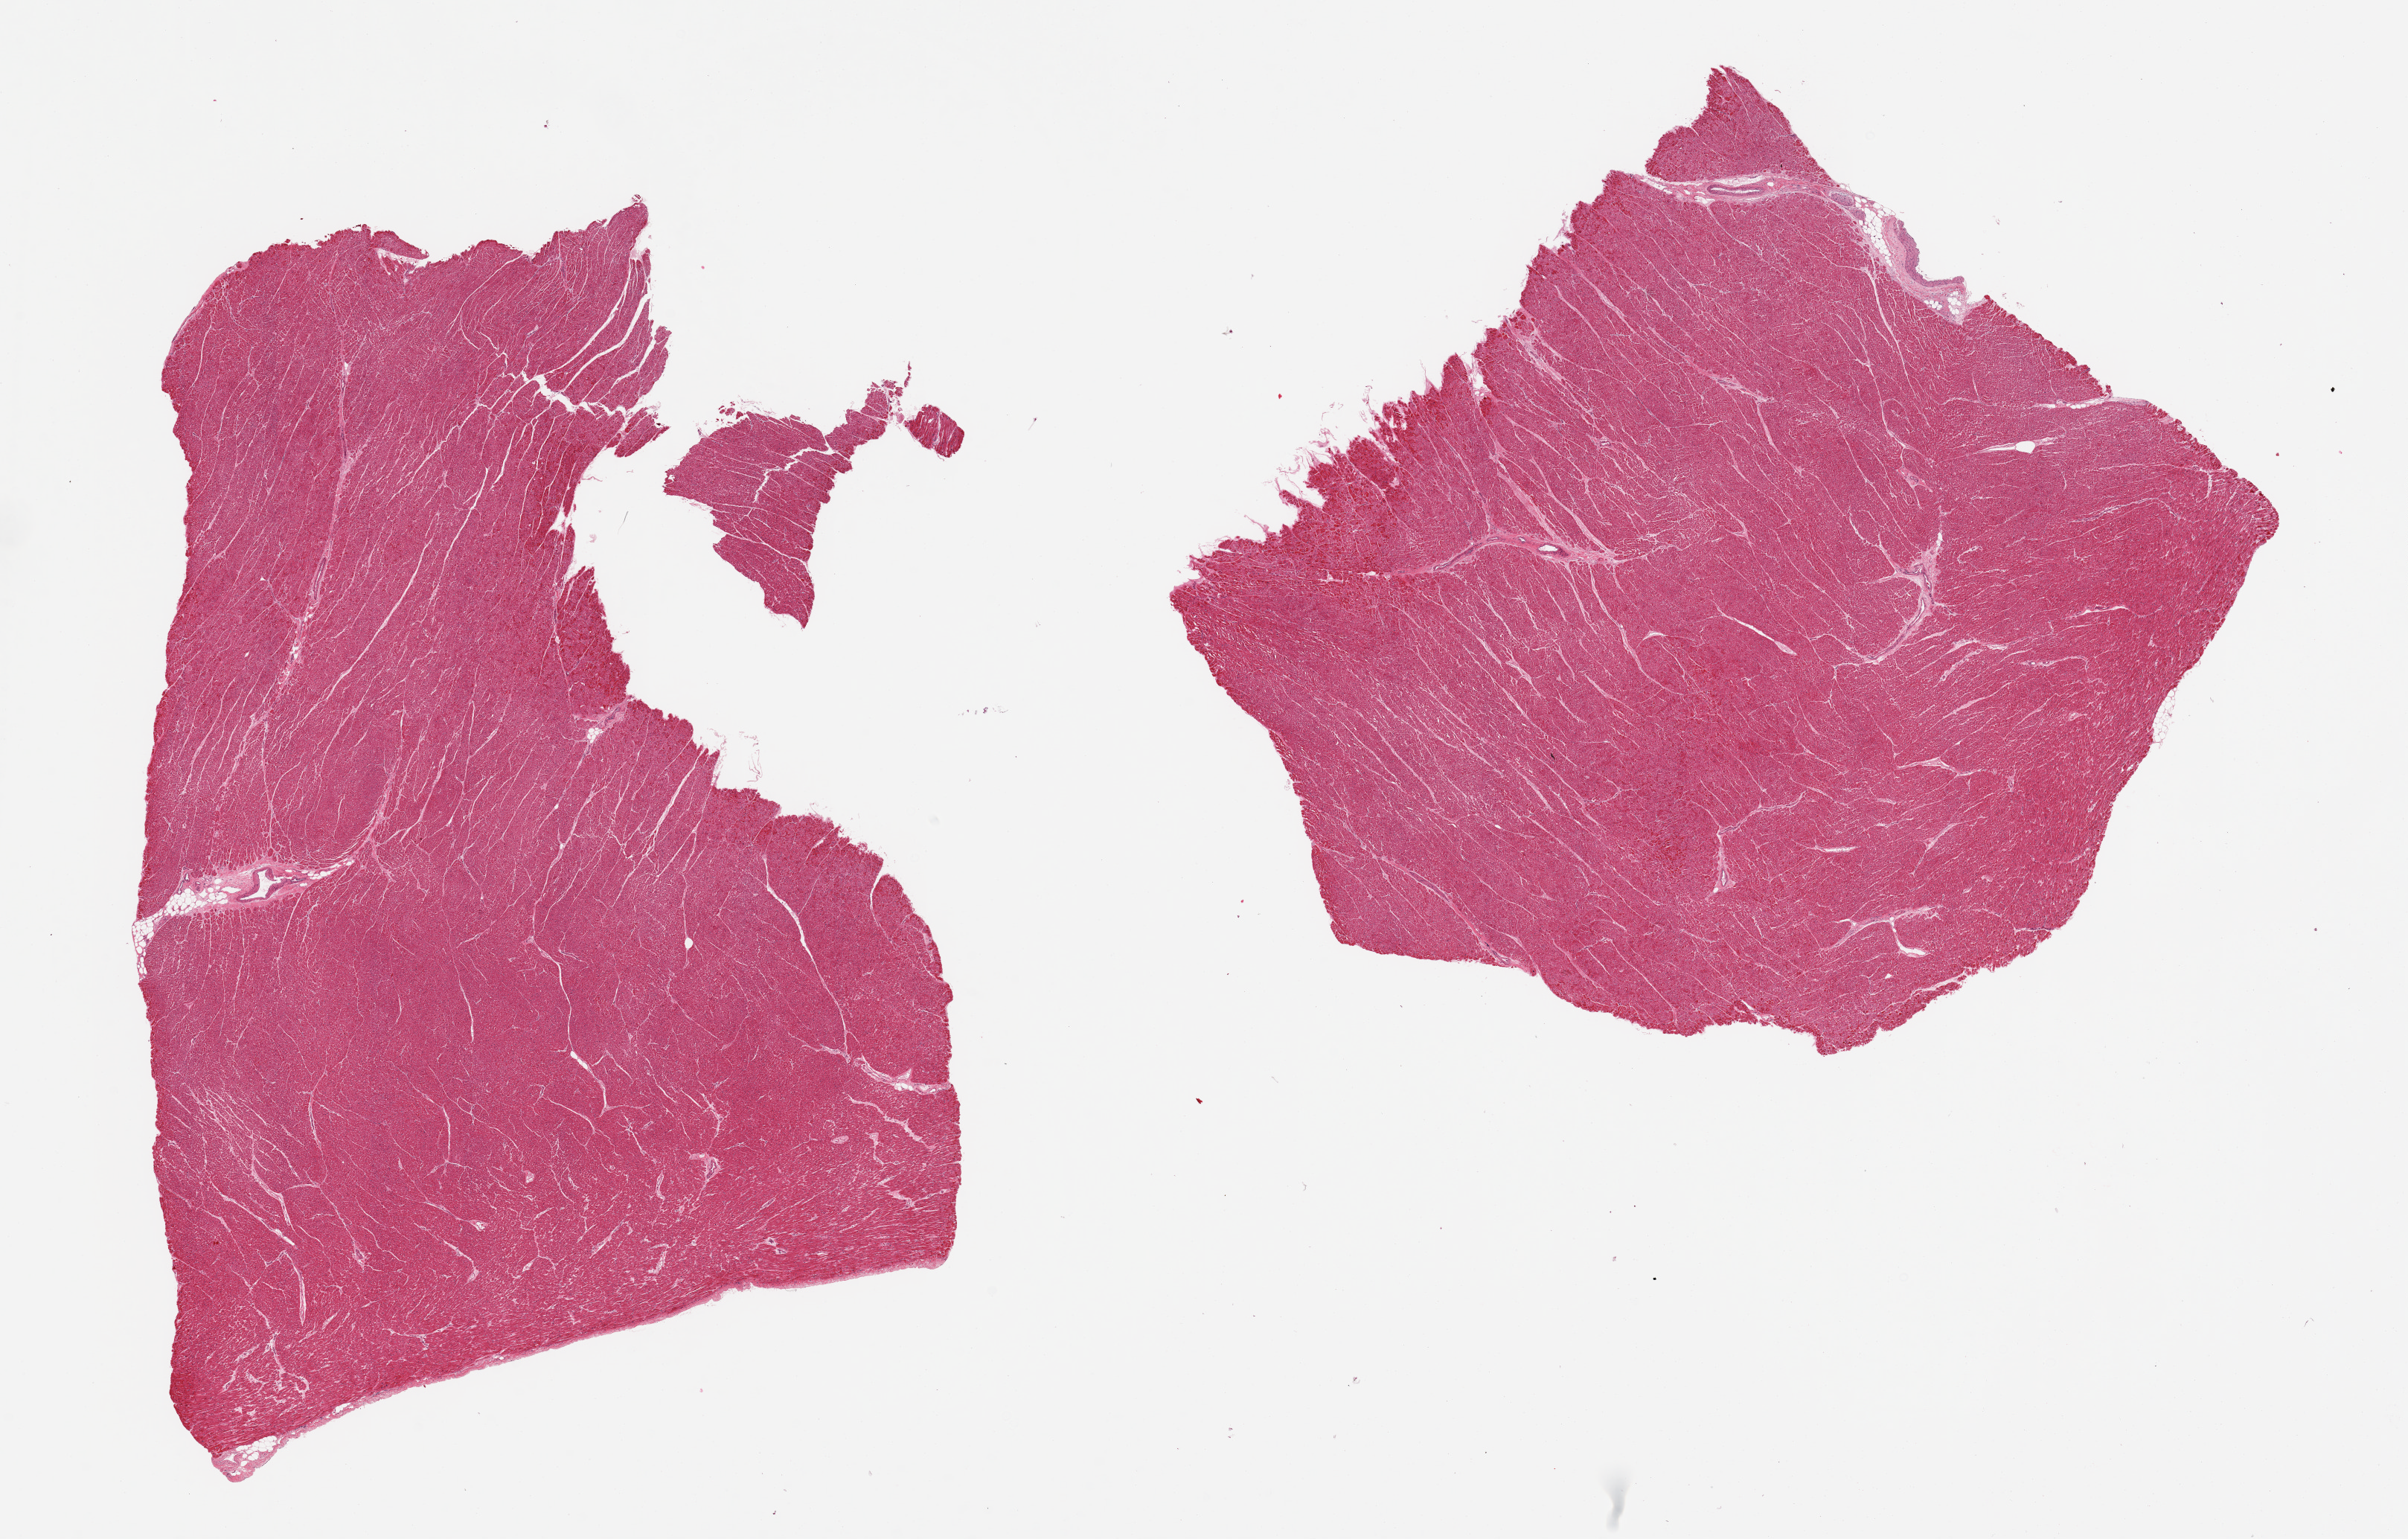
Haematoxylin and eosin whole-slide image, low-resolution overview of the scanned area, about 25.6 x 16.4 mm (from a 20x scan), PAXgene-fixed paraffin-embedded (PFPE) section, section of heart (target tissue), tissue donor sample. Male donor.
Review note (as recorded): 2 pieces. Hypertrophic fibers.